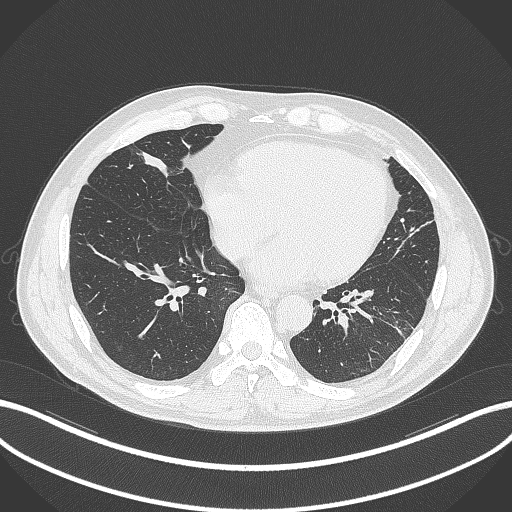
Chest CT, one axial slice; slice 92 of 399 in the series (ordered by position); 120 kVp; lung window (W 1500 / L -600 HU); 1 mm slice thickness; 512 × 512 image matrix, field of view 400 × 400 mm. Male patient, age 59 years. Case-level facts recorded for this patient, not image findings: clinical TNM (as recorded): T2a N1 M0.
Outlined on this slice (rectangle marked by the reading radiologist):
- lung tumour (recorded histology: adenocarcinoma): bounding box [x1, y1, x2, y2] px = [133, 147, 172, 189]